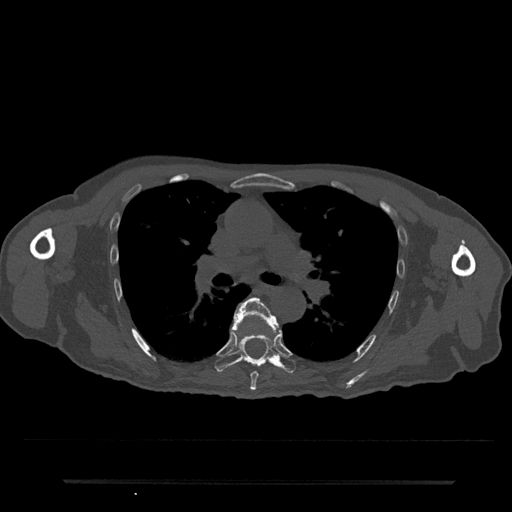
CT including the spine, one axial slice; slice 501 of 797 in the series (ordered by position); reconstruction kernel Br40s/3; 120 kVp; bone window (W 1800 / L 400 HU); 512 × 512 image matrix, field of view 427 × 427 mm. Male patient, age 74 years. From the clinical record (not read from this slice): primary cancer: prostate.
Outlined on this slice (semi-automatically segmented with operator editing):
- T6 vertebra: box from (x=231, y=297) to (x=279, y=391) px
- T7 vertebra: (x=215, y=329)–(x=296, y=373)